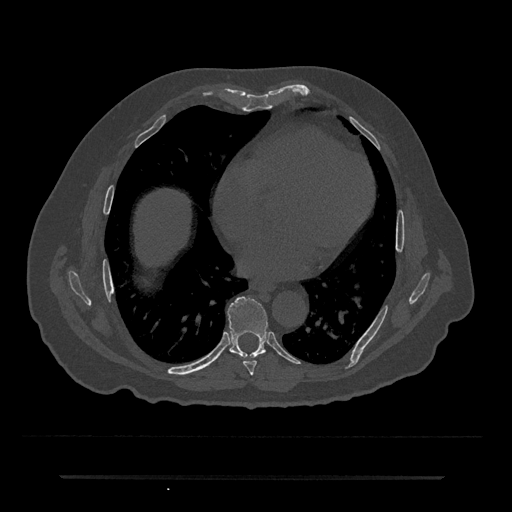
CT including the spine, one axial slice; position 356 of 797 along the scan axis; reconstruction kernel Br40s/3; 120 kVp; bone window (W 1800 / L 400 HU); 512 × 512 image matrix, field of view 437 × 437 mm. Male patient, age 69 years. From the clinical record (not read from this slice): primary cancer: prostate.
Outlined on this slice (semi-automatically segmented with operator editing):
- T7 vertebra: bounding box [x1, y1, x2, y2] px = [243, 354, 260, 375]
- T8 vertebra: [227, 297, 267, 358]